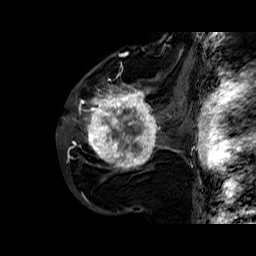
Breast MRI (dynamic contrast-enhanced), one sagittal slice. Slice 35 of 60 in the series (ordered by position). Dynamic contrast-enhanced series, time point 2 of 6 at this slice position (early post-contrast). 1.5 T. TE 6.4 ms, TR 32.8 ms. 256 × 256 image matrix, field of view 200 × 200 mm. Female patient. Case-level facts recorded for this patient, not image findings: setting: breast cancer imaged before/during neoadjuvant chemotherapy; receptor status: HR-positive, HER2-negative.
Outlined on this slice (semi-automatic segmentation, software-assisted and operator-edited):
- analysis volume of interest (the breast-tissue region the enhancement analysis was run in; not a lesion): bounding box <86,77,163,176> (left, top, right, bottom; pixels)
- tumour enhancement mask (voxels above the 100 % enhancement threshold inside the analysis volume of interest): <86,78,160,170>